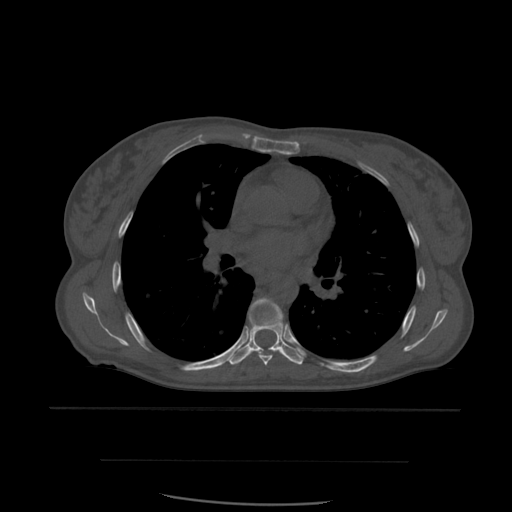
CT including the spine, one axial slice; slice 382 of 574 in the series (ordered by position); bone window (W 1800 / L 400 HU); 1.25 mm slice thickness; 512 × 512 image matrix, field of view 392 × 392 mm. Patient age 48 years. From the clinical record (not read from this slice): primary cancer: lung; vertebrae with lytic lesions (as recorded): T11.
Structures marked on this image (semi-automatically segmented with operator editing):
- T6 vertebra: bounding box [x1, y1, x2, y2] px = [249, 298, 281, 366]
- T7 vertebra: [230, 302, 303, 366]